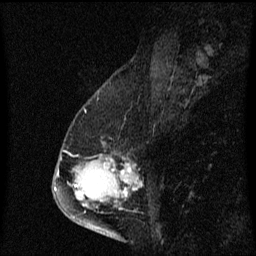
Breast MRI (dynamic contrast-enhanced), one sagittal slice. Position 26 of 60 along the scan axis. Dynamic contrast-enhanced series, image 2 of 3 at this slice position (ordered by acquisition). 1.5 T. TE 4.2 ms, TR 8.4 ms. 2 mm slice thickness. 256 × 256 image matrix, field of view 200 × 200 mm. Patient: female, 57 years. From the clinical record (not read from this slice): setting: breast cancer imaged before/during neoadjuvant chemotherapy; receptor status: HR-positive, HER2-negative.
Annotated regions visible in this slice (semi-automatic segmentation, software-assisted and operator-edited):
- analysis volume of interest (the breast-tissue region the enhancement analysis was run in; not a lesion): bounding box <73,142,129,177> (left, top, right, bottom; pixels)
- tumour enhancement mask (voxels above the 70 % enhancement threshold inside the analysis volume of interest): <112,168,129,173>